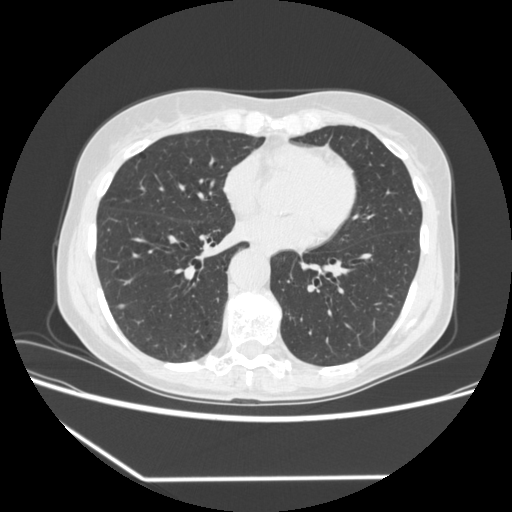
Low-dose screening chest CT, one axial slice. Position 158 of 323 along the scan axis. Reconstruction kernel STANDARD. 120 kVp. Lung window (W 1500 / L -600 HU). 512 × 512 image matrix.
Outlined on this slice (outlined manually by an expert reader):
- lesion 2 (nodule, lower lobe of right lung): bounding box (x1, y1, x2, y2) in pixels: (119, 304, 125, 308)